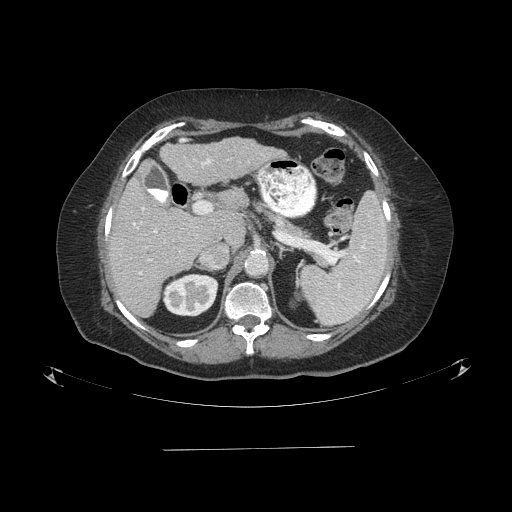
Contrast-enhanced abdominal CT (liver protocol), one axial slice. Slice 50 of 103 in the series (ordered by position). Reconstruction kernel STANDARD. 120 kVp. One of 2 acquisitions stored at this slice position. Soft-tissue window (W 400 / L 40 HU). 2.5 mm slice thickness. 512 × 512 image matrix, field of view 500 × 500 mm. Case-level facts recorded for this patient, not image findings: diagnosis: hepatocellular carcinoma (patient treated with transarterial chemoembolisation; whether this scan precedes or follows treatment is not stated here); TNM stage (as recorded): Stage-IIIA; Child-Pugh class: A; tumour differentiation: poorly differentiated; tumour size: 5.2 cm.
Outlined on this slice (semi-automatic segmentation, software-assisted and operator-edited):
- liver parenchyma outside the tumour (the mass and vessels are separate outlines, so this box may not span the whole liver): bounding box (x1, y1, x2, y2) in pixels: (108, 136, 282, 316)
- liver vessels: (133, 159, 211, 275)